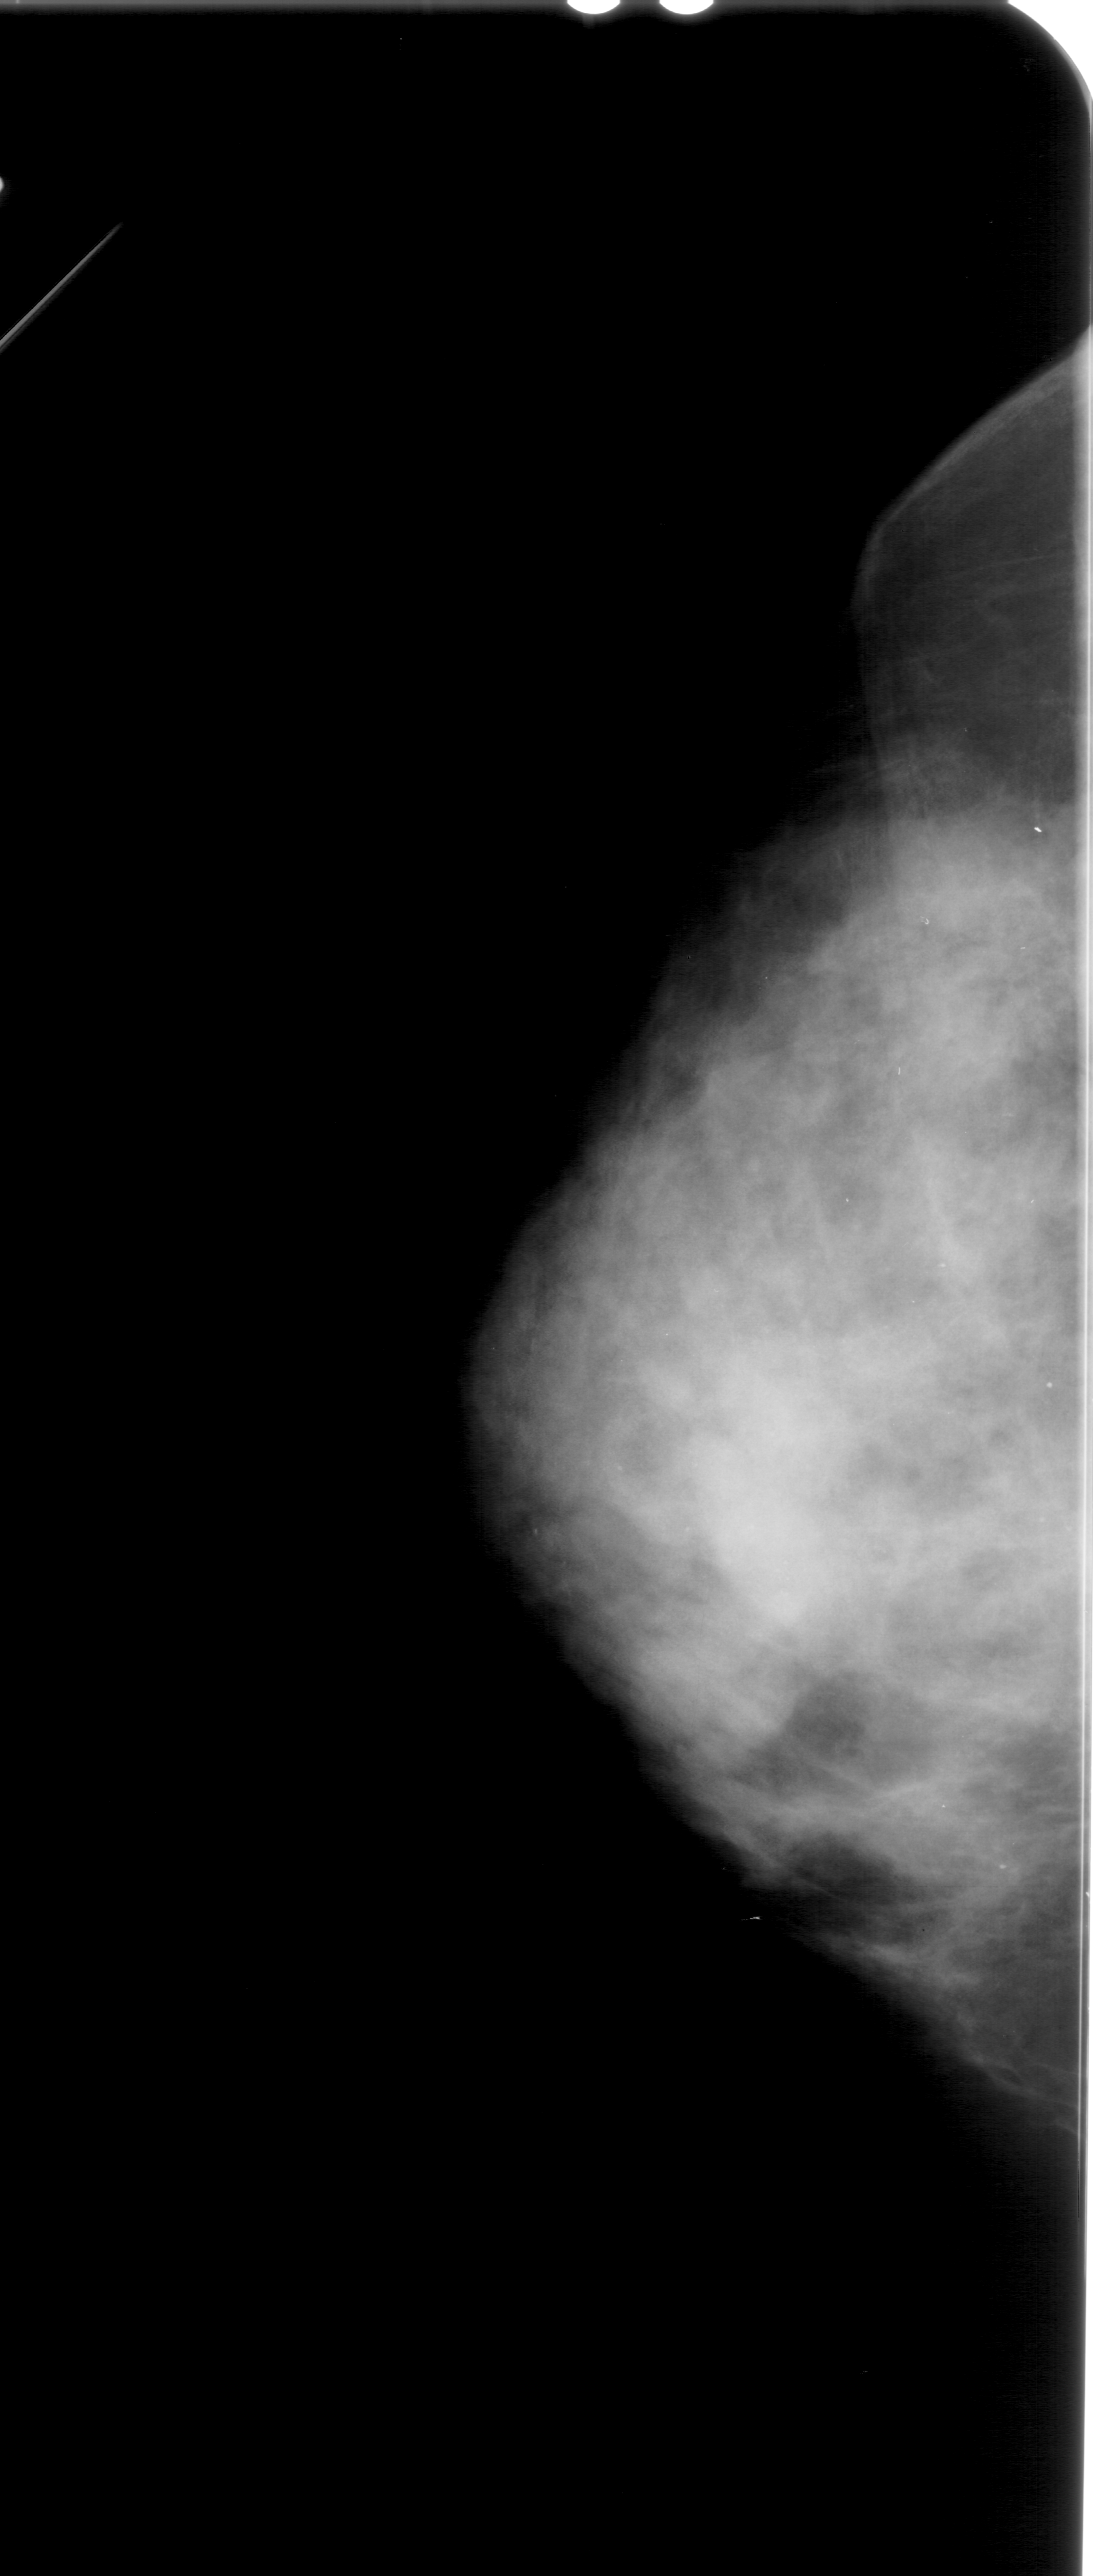
Mammogram (digitized film). Left breast. Craniocaudal (CC) view. Breast composition: extremely dense (BI-RADS density category 4 of 4). 1093 × 2576 image matrix.
Expert-marked regions of interest on this film, with their recorded descriptors:
- calcifications, morphology punctate, distribution segmental; BI-RADS assessment category 4; subtlety rating 2 on a 1 (subtle) to 5 (obvious) scale; pathology (as recorded): malignant: bounding box [x1, y1, x2, y2] px = [594, 1224, 967, 1552]